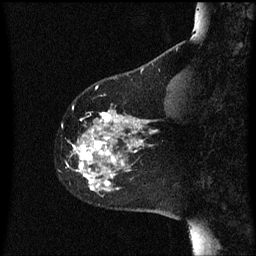
Breast MRI (dynamic contrast-enhanced), one sagittal slice; position 16 of 60 along the scan axis; dynamic contrast-enhanced series, image 2 of 3 at this slice position (ordered by acquisition); 1.5 T; TE 4.2 ms, TR 8 ms; 2 mm slice thickness; 256 × 256 image matrix, field of view 200 × 200 mm. Female patient, age 60 years.
Annotated regions visible in this slice (semi-automatically segmented with operator editing):
- analysis volume of interest (the breast-tissue region the enhancement analysis was run in; not a lesion): bounding box <68,104,158,197> (left, top, right, bottom; pixels)
- tumour enhancement mask (voxels above the 70 % enhancement threshold inside the analysis volume of interest): <73,110,158,191>